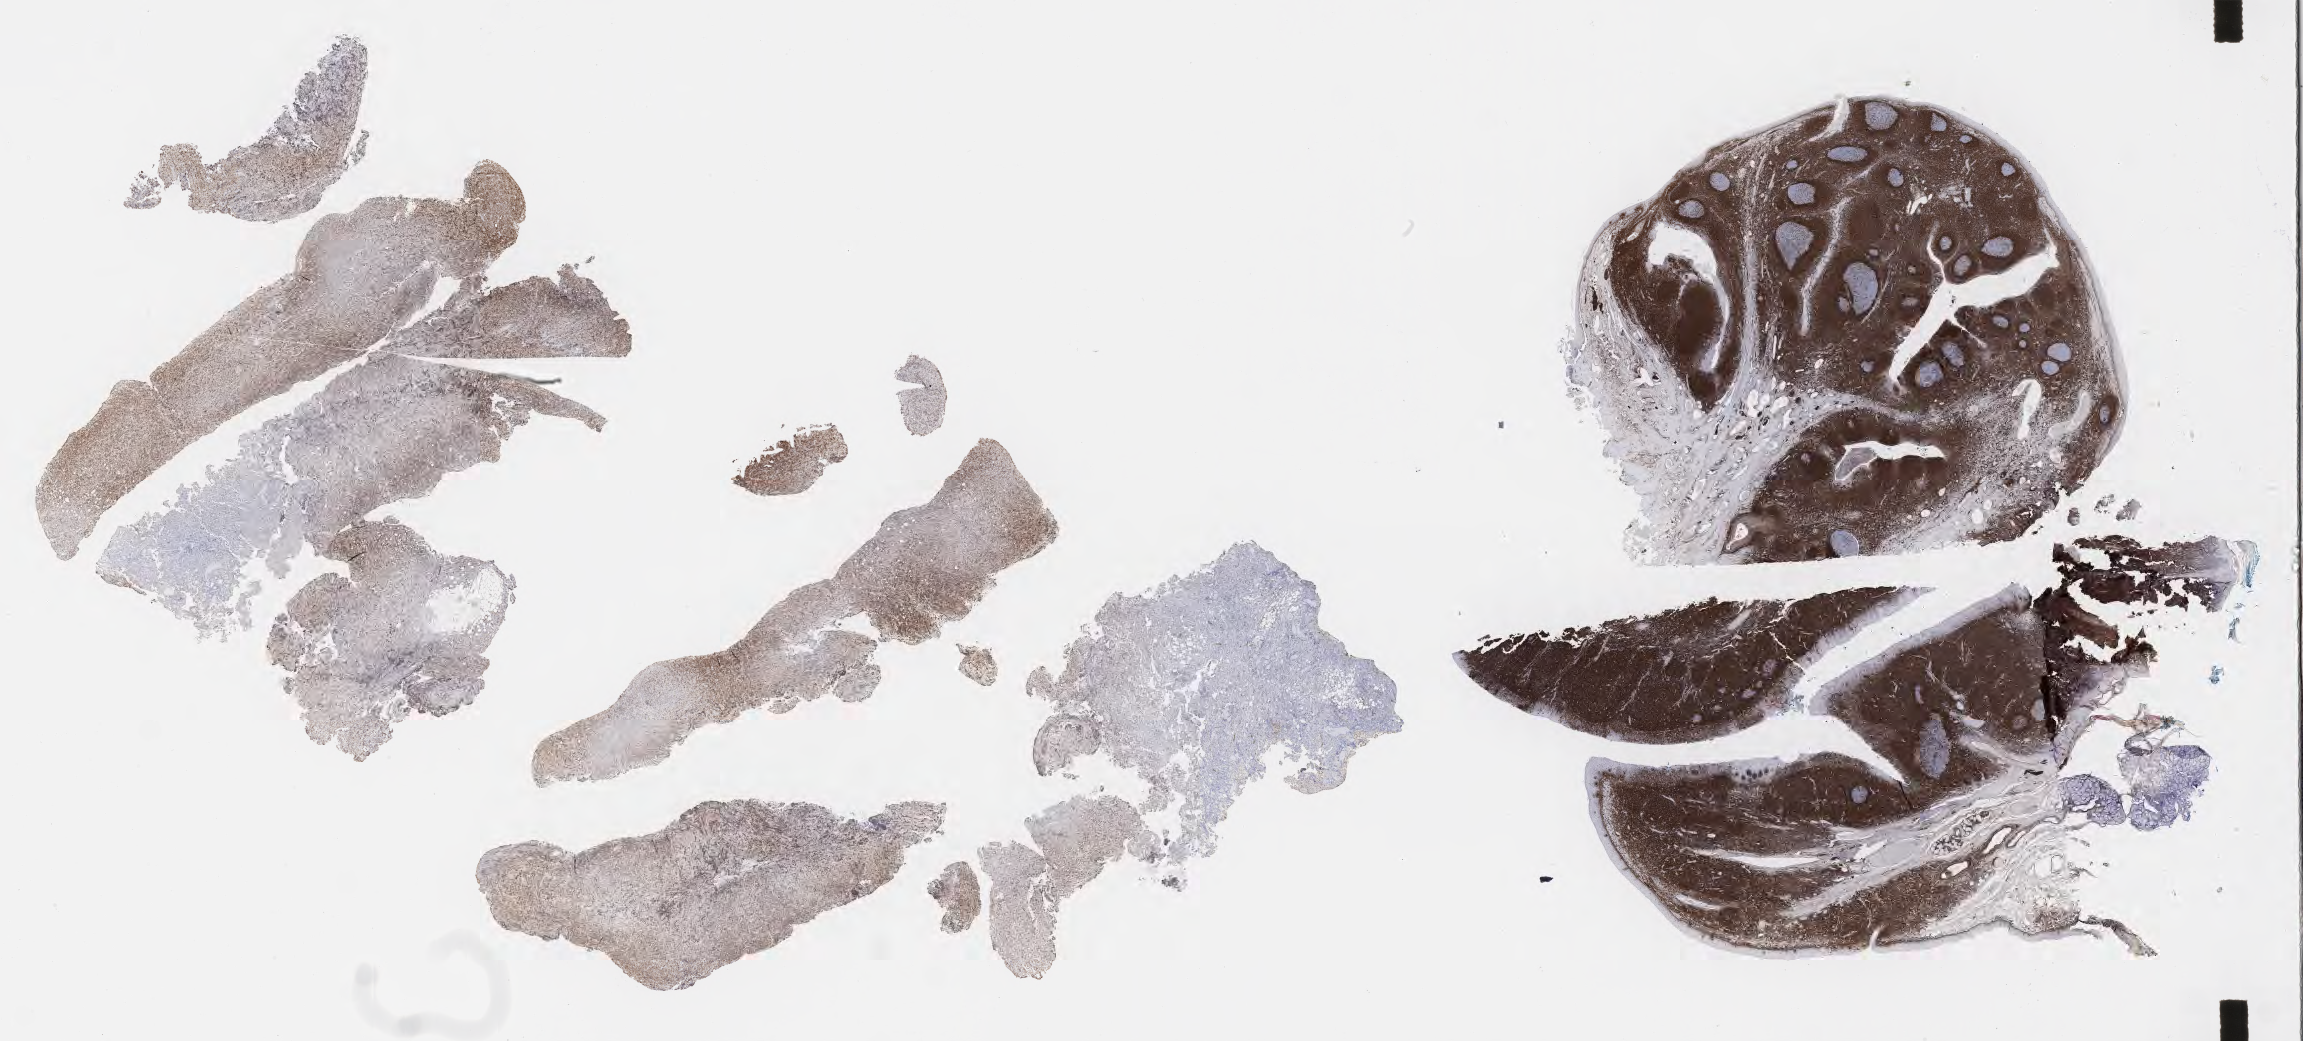
Immunohistochemistry (IHC) whole-slide image stained for BCL2 — a low-resolution overview of the entire scanned area, about 37.2 x 16.8 mm. Specimen: tumor tissue. Patient: male, 45 years old.
Histologic diagnosis: Diffuse large B-cell lymphoma, NOS.